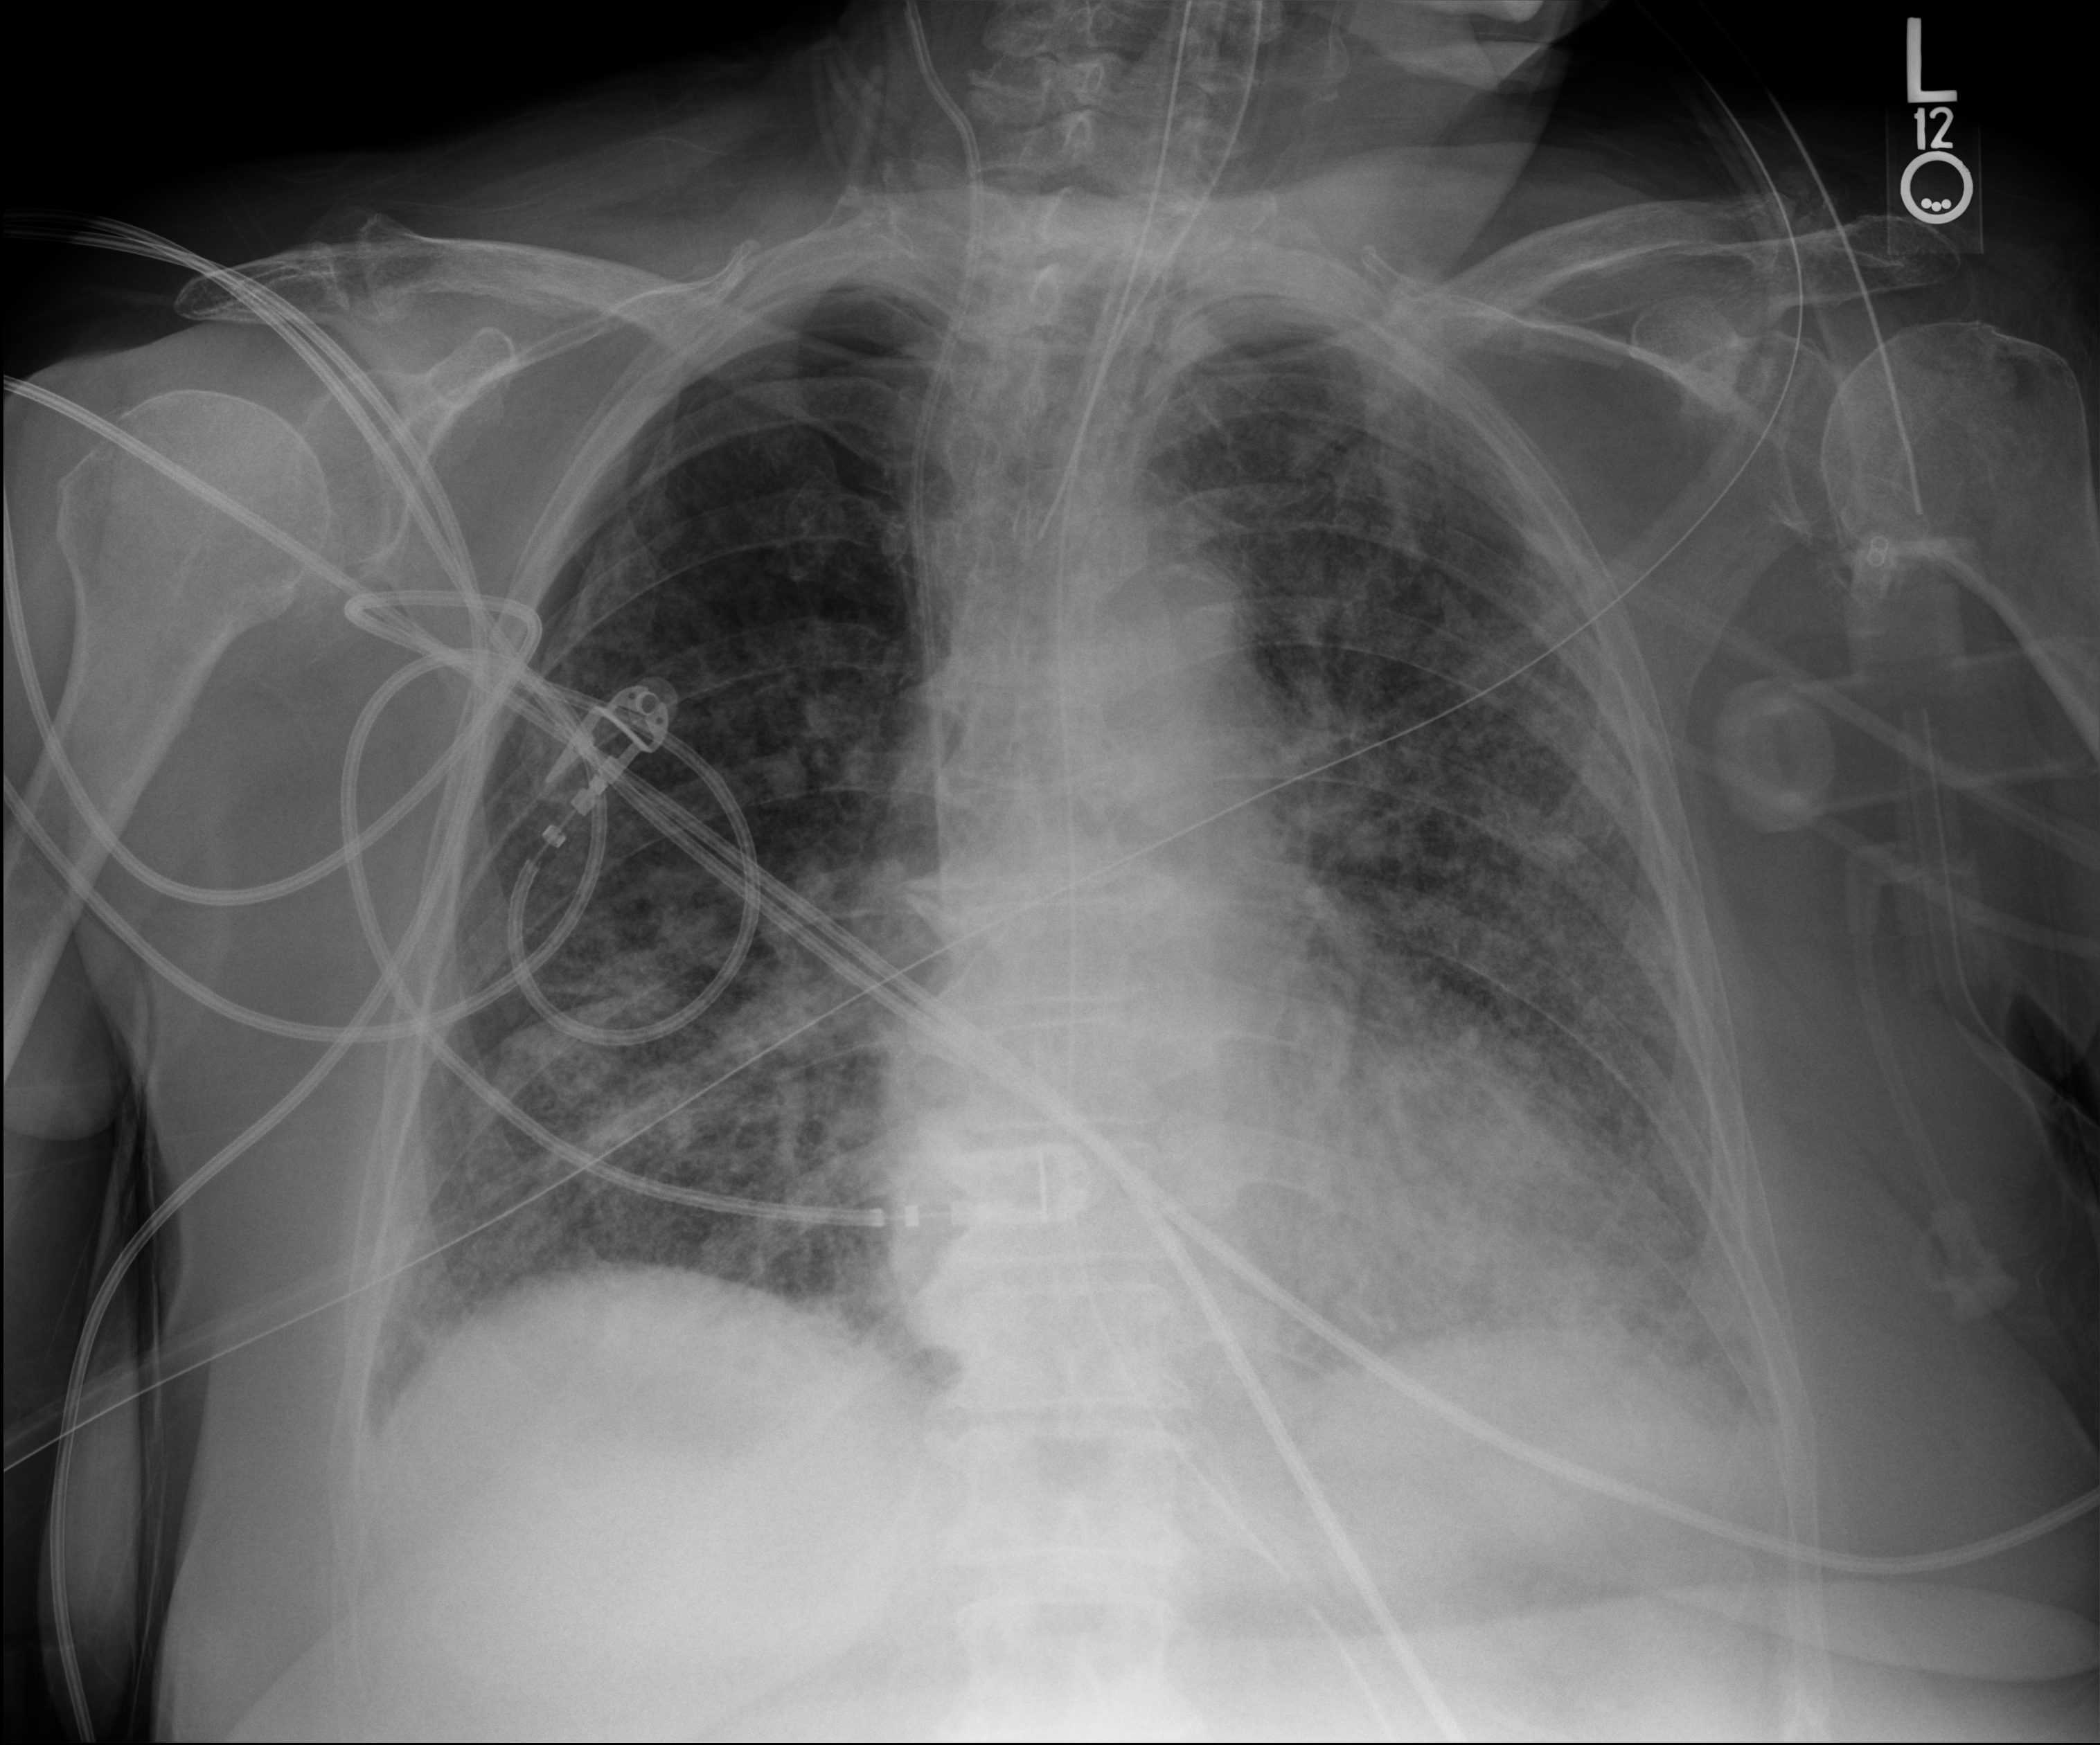
Chest X-ray (portable). Patient hospitalised with COVID-19; female, aged 75–90 years.
Hospital-stay facts (about this admission, not read from this image; timing relative to this image not recorded): mechanically ventilated during this hospital stay: yes.